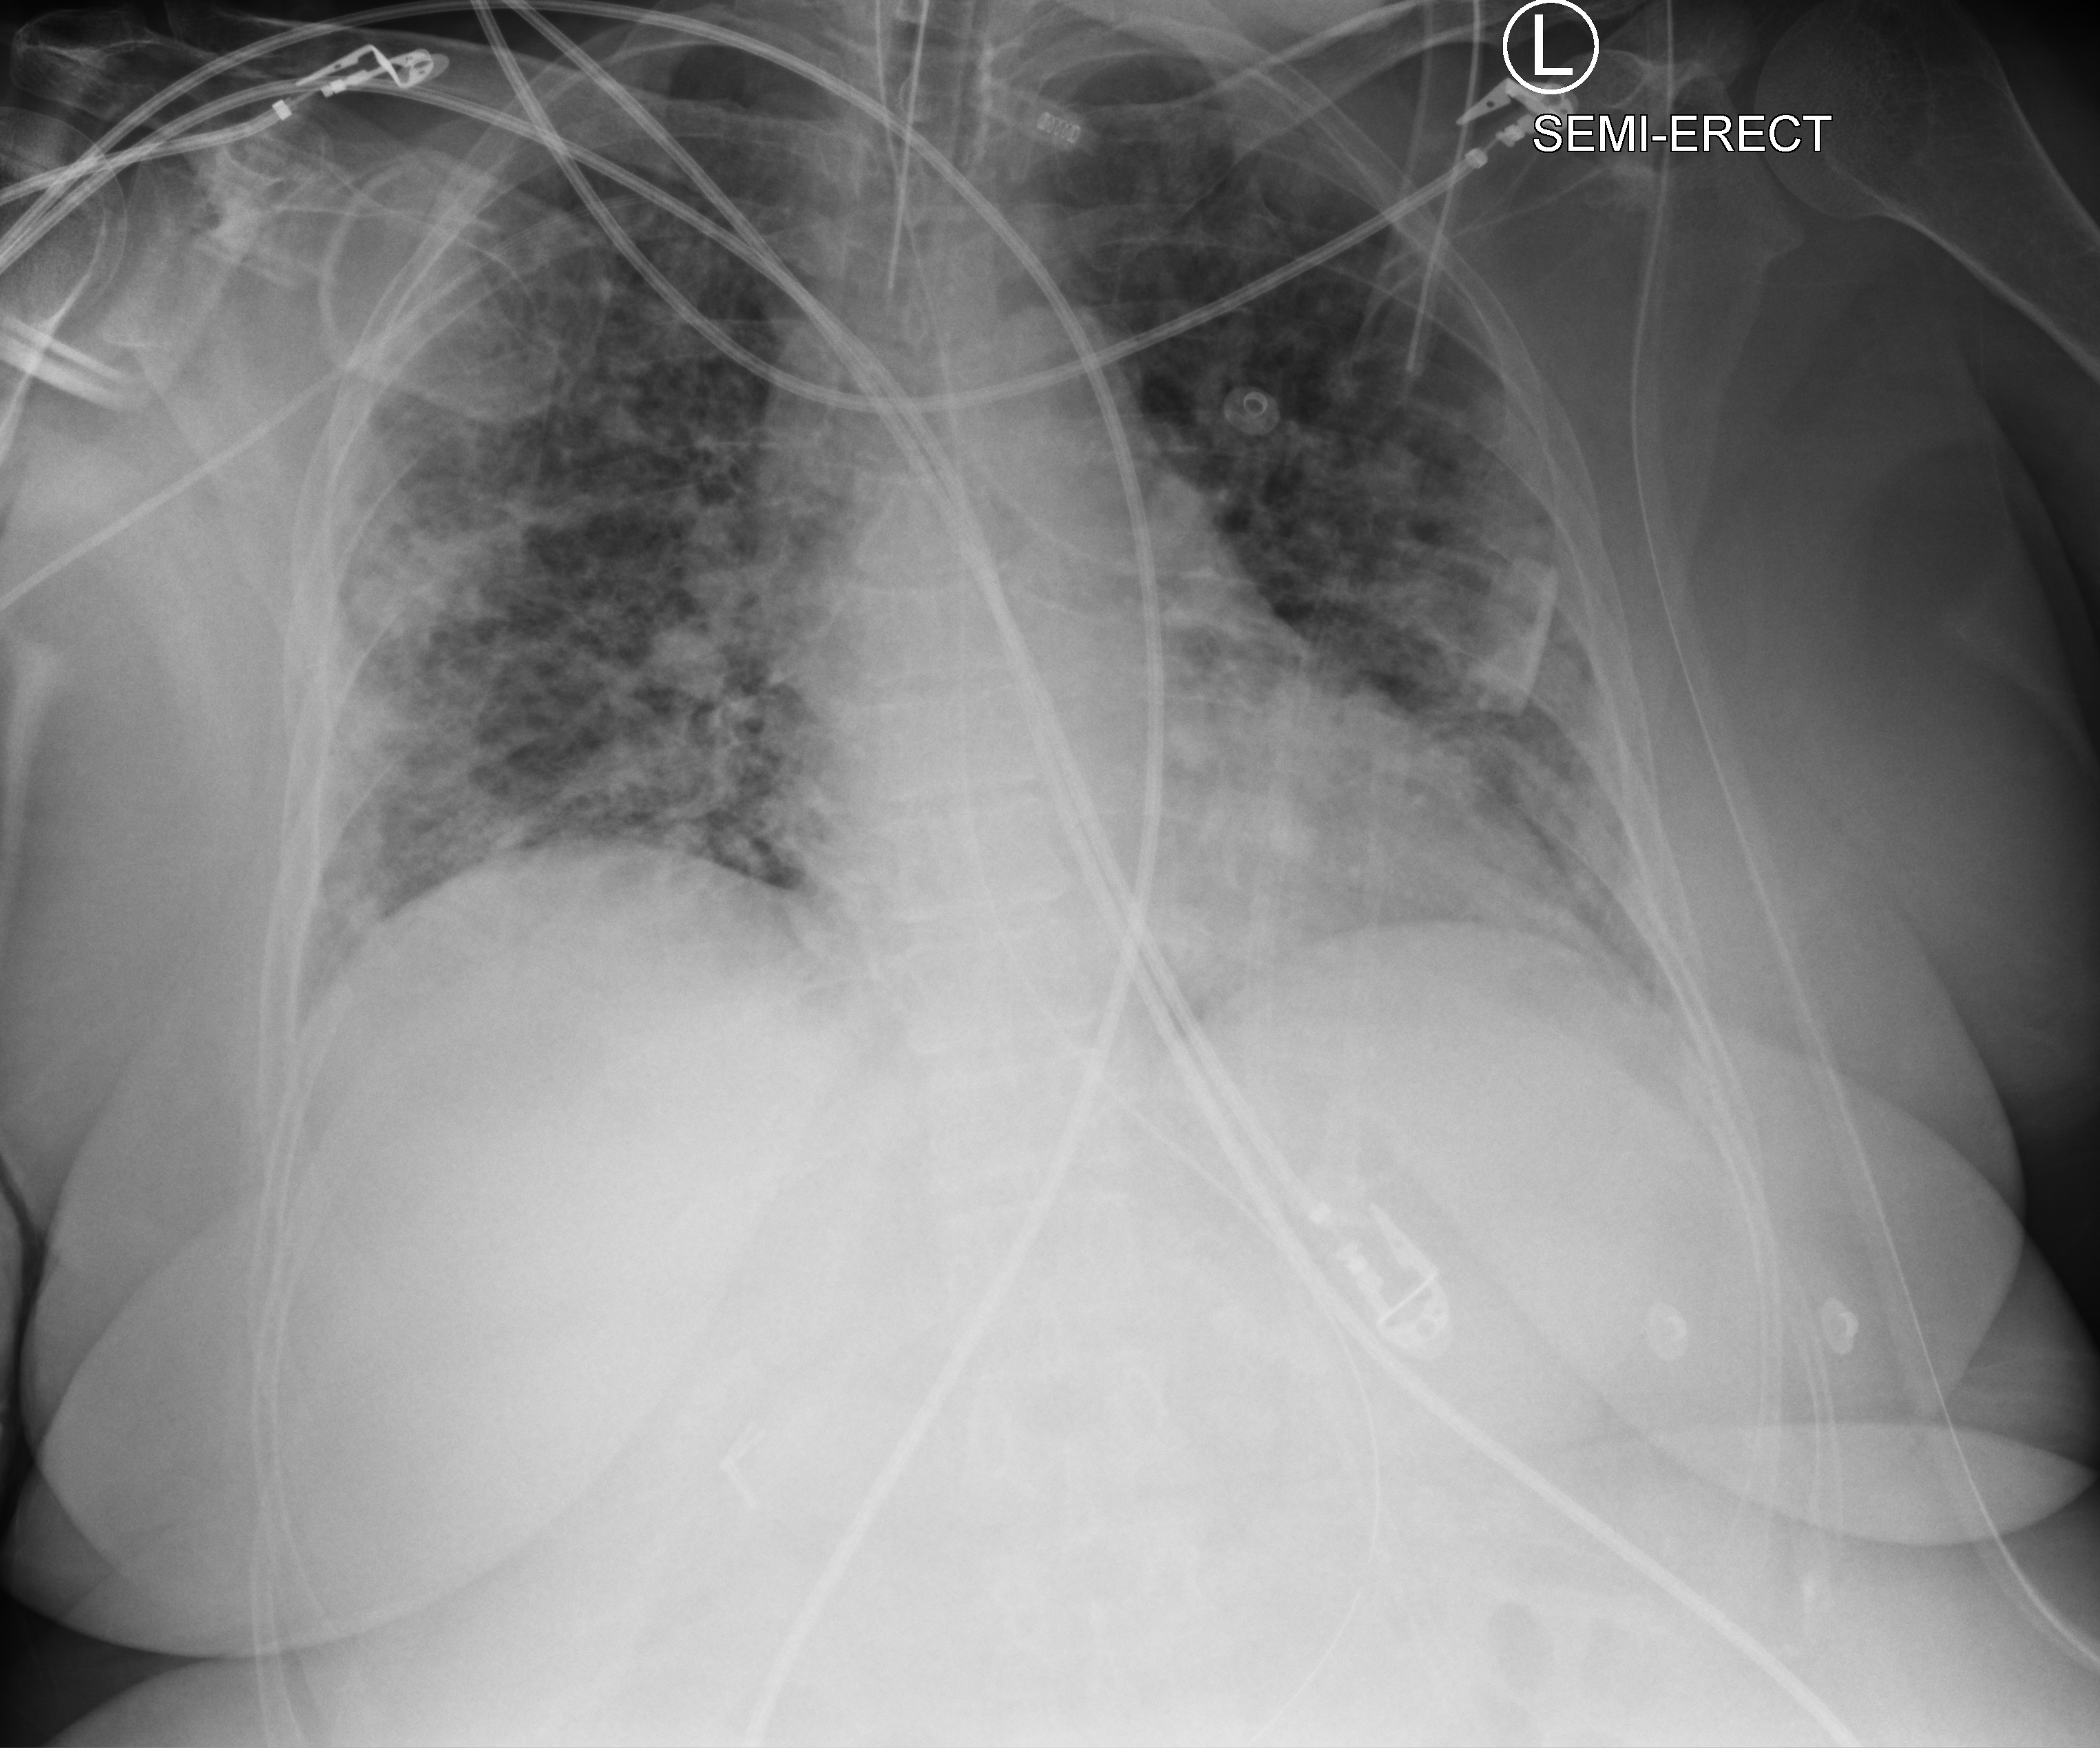
Bedside chest radiograph (computed radiography). Female patient hospitalised with COVID-19, age 18–59 years.
Admission-level facts for this patient (not findings on this image; timing relative to this image not recorded): other chronic lung disease (admission record): no; admitted to intensive care during this hospital stay: yes.